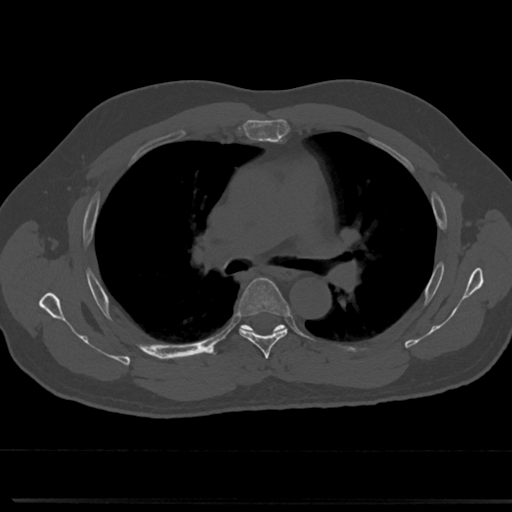
CT including the spine, one axial slice. Slice 488 of 817 in the series (ordered by position). 120 kVp. Bone window (W 1800 / L 400 HU). 0.5 mm slice thickness. 512 × 512 image matrix, field of view 355 × 355 mm. Patient: male, 61 years. Case-level facts recorded for this patient, not image findings: primary cancer: prostate.
Structures marked on this image (semi-automatic segmentation, software-assisted and operator-edited):
- T4 vertebra: bounding box <265,365,273,374> (left, top, right, bottom; pixels)
- T5 vertebra: <234,278,291,350>
- T6 vertebra: <243,327,282,329>